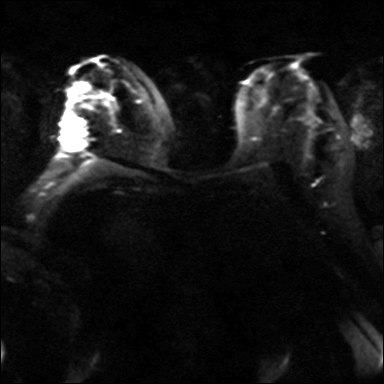
Breast MRI, one axial slice. Diffusion-weighted series; image 2 of 4 stored at this slice position (different b-values; order by instance number). 3 T. 4 mm slice thickness. 384 × 384 image matrix. Female patient.
Annotated regions visible in this slice (outlined manually by an expert reader):
- tumour on diffusion-weighted imaging: bounding box <66,122,83,150> (left, top, right, bottom; pixels)